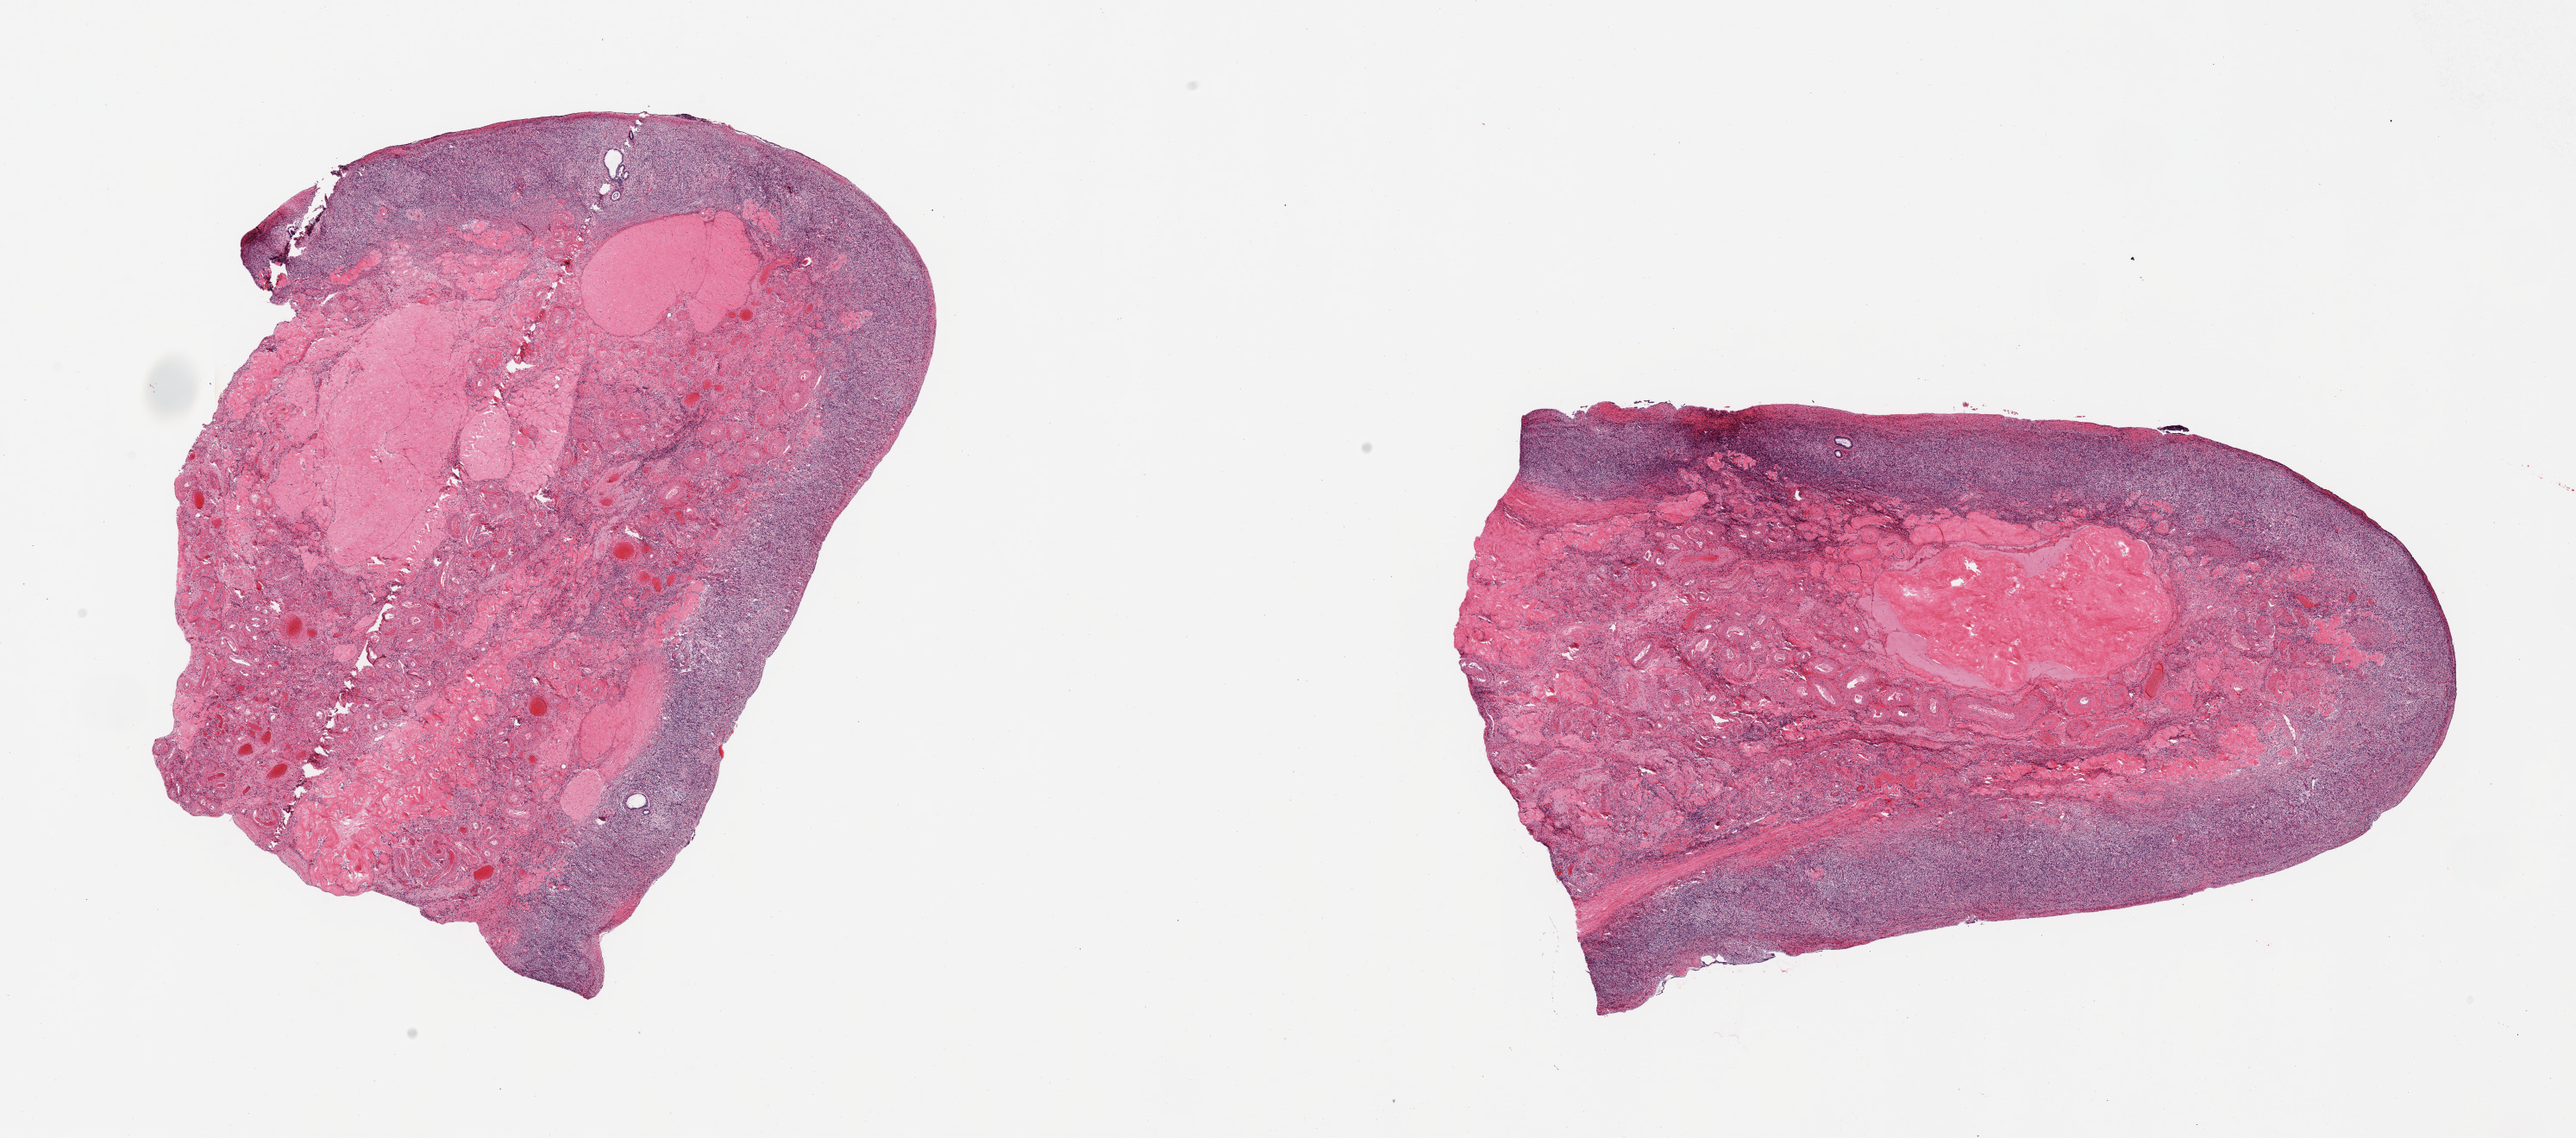
Digitized hematoxylin and eosin (H&E)-stained section, brightfield, shown as a low-resolution overview of the whole scanned area (about 23.6 x 10.4 mm, from a 20x scan). PAXgene-fixed paraffin-embedded (PFPE) section. Section of ovary (target tissue). Tissue donor sample. Donor sex: female.
Pathologist's review note for this sample: 2 pieces; a few small follicles in outer rim; core contains corpora albicantia & vessels.